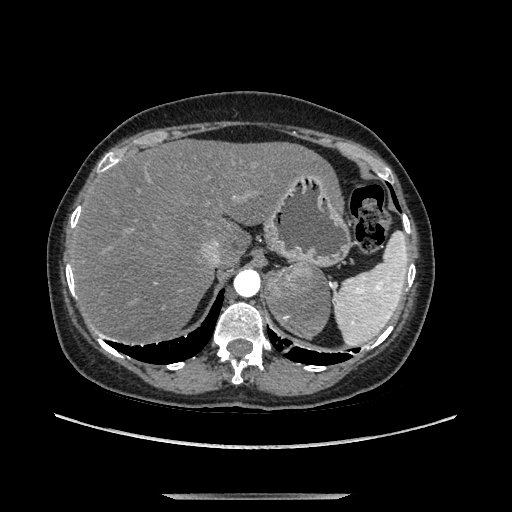
Contrast-enhanced abdominal CT, one axial slice; position 103 of 169 along the scan axis; soft-tissue window (W 400 / L 40 HU); 1.25 mm slice thickness; 512 × 512 image matrix, field of view 400 × 400 mm. Female patient. From the clinical record (not read from this slice): diagnosis: adrenocortical carcinoma; tumour side: left adrenal; tumour size at pathology: 9 cm; Ki-67 index: 2 %; stage (as recorded): 3.
Outlined on this slice (semi-automatically segmented with operator editing):
- mass: box from (x=266, y=264) to (x=330, y=335) px